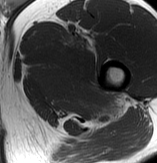
MRI of an extremity soft-tissue mass, one axial slice. MR volume resampled by the dataset authors to the PET/CT grid (not the native acquisition matrix). 3.27 mm slice thickness. 157 × 163 image matrix, field of view 153 × 159 mm. Male patient. From the clinical record (not read from this slice): histological type: extraskeletal osteosarcoma; grade: high; site of the primary tumour: left adductur.
Annotated regions visible in this slice (expert contour drawn on MRI and transferred to this co-registered scan by the dataset authors):
- gross tumour volume (mass): bounding box [x1, y1, x2, y2] px = [26, 24, 130, 125]